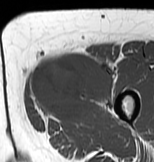
MRI of an extremity soft-tissue mass, one axial slice. Slice 24 of 83 in the series (ordered by position). MR volume resampled by the dataset authors to the PET/CT grid (not the native acquisition matrix). 3.27 mm slice thickness. 154 × 162 image matrix, field of view 150 × 158 mm. Female patient. From the clinical record (not read from this slice): histological type: myxofibrosarcoma; grade: intermediate; site of the primary tumour: left thigh.
Annotated regions visible in this slice (expert contour drawn on MRI and transferred to this co-registered scan by the dataset authors):
- gross tumour volume including surrounding oedema: bounding box [x1, y1, x2, y2] px = [28, 48, 116, 124]
- gross tumour volume (mass): [30, 54, 114, 119]